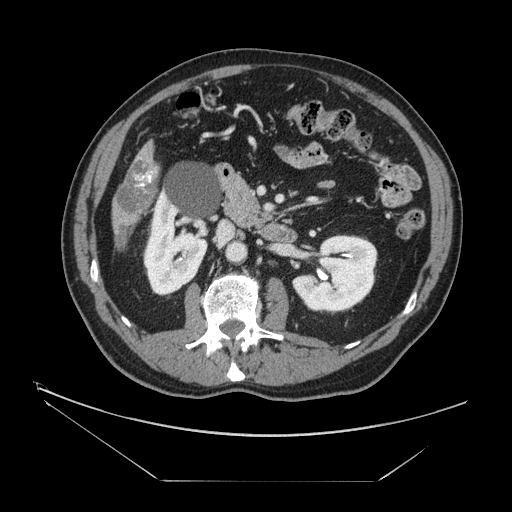
Contrast-enhanced abdominal CT, one axial slice; position 55 of 161 along the scan axis; intravenous contrast given; soft-tissue window (W 400 / L 40 HU); 2.5 mm slice thickness; 512 × 512 image matrix, field of view 440 × 440 mm. Male patient, age 65 years. Case-level facts recorded for this patient, not image findings: diagnosis: colorectal cancer liver metastases, imaged before liver resection; multiple liver metastases: yes; largest metastasis: 4.2 cm; chemotherapy before resection: yes.
Outlined on this slice (expert manual segmentation):
- liver: bounding box (x1, y1, x2, y2) in pixels: (113, 144, 158, 232)
- portal vein (with intrahepatic branches): (135, 171, 154, 186)
- liver metastasis: (119, 230, 128, 249)
- liver metastasis: (117, 161, 159, 217)